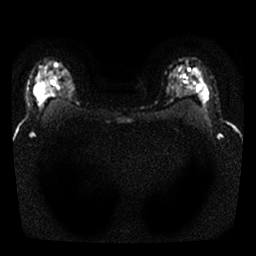
Breast MRI, one axial slice; slice 20 of 25 in the series (ordered by position); diffusion-weighted series; image 2 of 4 stored at this slice position (different b-values; order by instance number); 1.5 T; 4 mm slice thickness; 256 × 256 image matrix. Female patient.
Outlined on this slice (outlined manually by an expert reader):
- tumour on diffusion-weighted imaging: bounding box <36,63,60,102> (left, top, right, bottom; pixels)